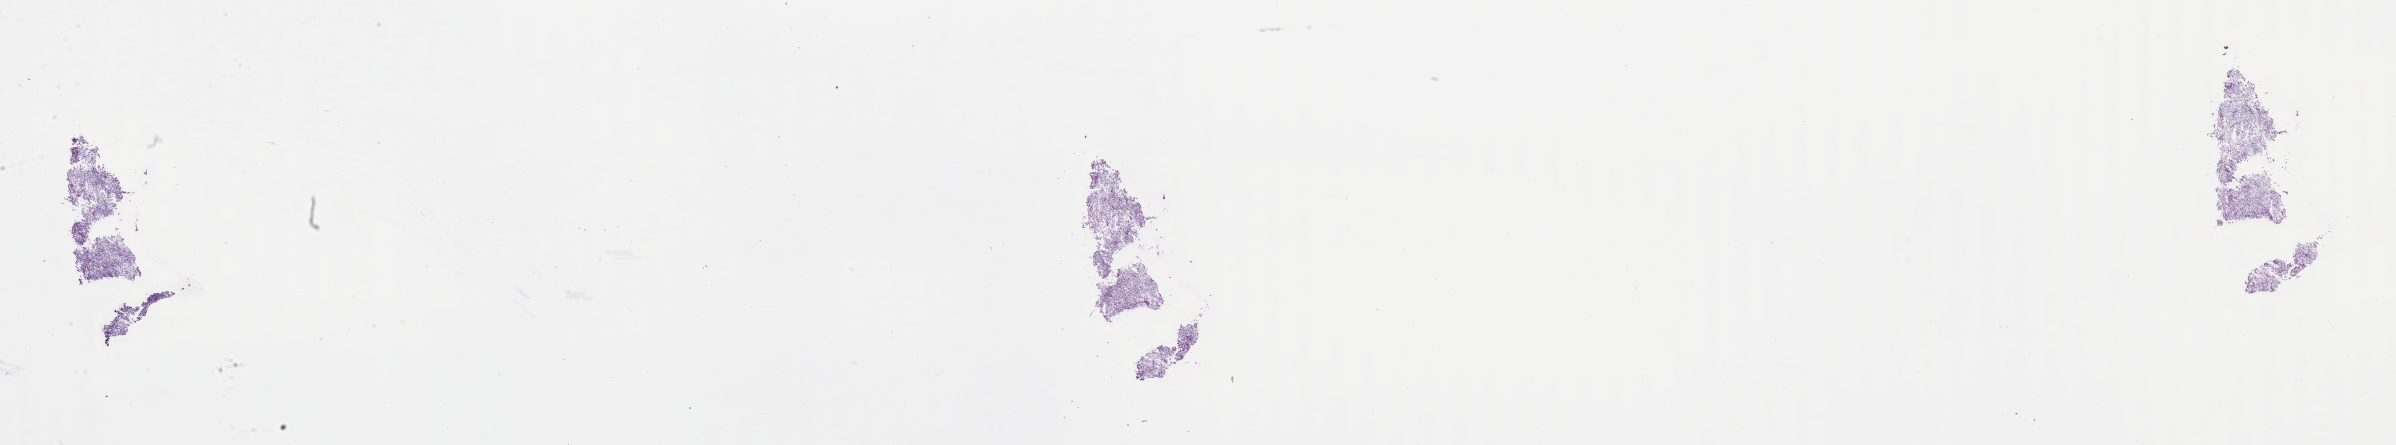
Digitized hematoxylin and eosin (H&E)-stained section of tumor tissue from the cerebellum, low-resolution overview of the scanned area, about 38.7 x 7.2 mm. Frozen section. Patient: female, age 157 months (13 years 1 month).
Recorded diagnosis: Atypical teratoid/rhabdoid tumor.